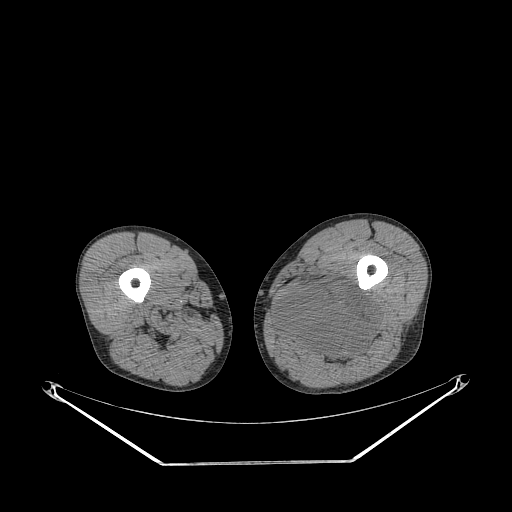
CT of an extremity soft-tissue mass (from a PET/CT study), one axial slice. Position 238 of 267 along the scan axis. Reconstruction kernel STANDARD. 140 kVp. Soft-tissue window (W 400 / L 40 HU). 3.75 mm slice thickness. 512 × 512 image matrix. Male patient. Case-level facts recorded for this patient, not image findings: histological type: undifferentiated pleomorphic liposarcoma; grade: high; site of the primary tumour: left thigh.
Structures marked on this image (expert contour drawn on MRI and transferred to this co-registered scan by the dataset authors):
- gross tumour volume including surrounding oedema: bounding box (x1, y1, x2, y2) in pixels: (276, 281, 378, 362)
- gross tumour volume (mass): (276, 281, 378, 359)